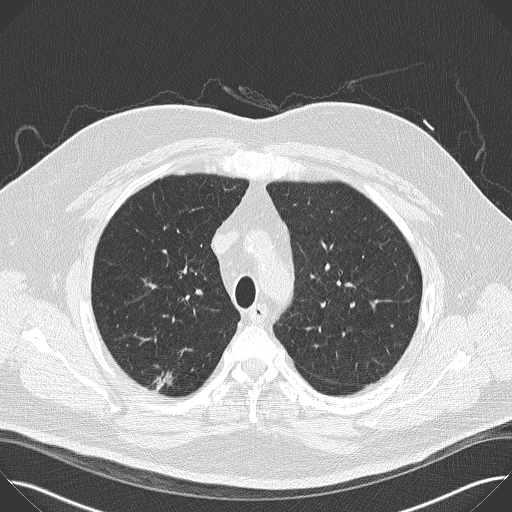
Low-dose screening chest CT, one axial slice; position 123 of 160 along the scan axis; 120 kVp; lung window (W 1500 / L -600 HU); 512 × 512 image matrix, field of view 380 × 380 mm.
Outlined on this slice (expert manual segmentation):
- lesion 1 (tumor, upper lobe of right lung): bounding box (x1, y1, x2, y2) in pixels: (152, 372, 173, 393)